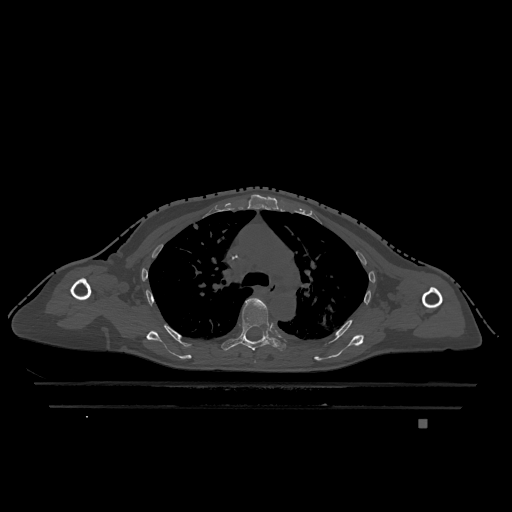
CT including the spine, one axial slice. Slice 843 of 1317 in the series (ordered by position). Bone window (W 1800 / L 400 HU). 0.5 mm slice thickness. 512 × 512 image matrix, field of view 500 × 500 mm. Patient: female, 74 years. Case-level facts recorded for this patient, not image findings: primary cancer: lung; vertebrae with lytic lesions (as recorded): T1, T4, T5, T6, L4, L5.
Annotated regions visible in this slice (semi-automatic segmentation, software-assisted and operator-edited):
- T5 vertebra: bounding box <221,298,286,352> (left, top, right, bottom; pixels)